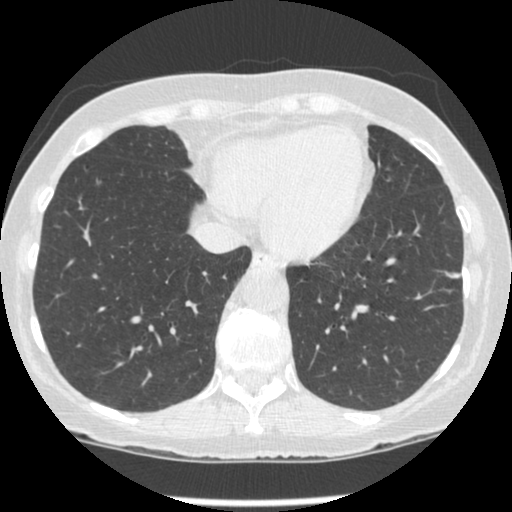
Low-dose screening chest CT, one axial slice; slice 71 of 247 in the series (ordered by position); reconstruction kernel STANDARD; 120 kVp; lung window (W 1500 / L -600 HU); 512 × 512 image matrix, field of view 303 × 303 mm.
Structures marked on this image (manually delineated by an expert):
- lesion 1 (tumor, lower lobe of left lung): bounding box [x1, y1, x2, y2] px = [446, 272, 460, 279]